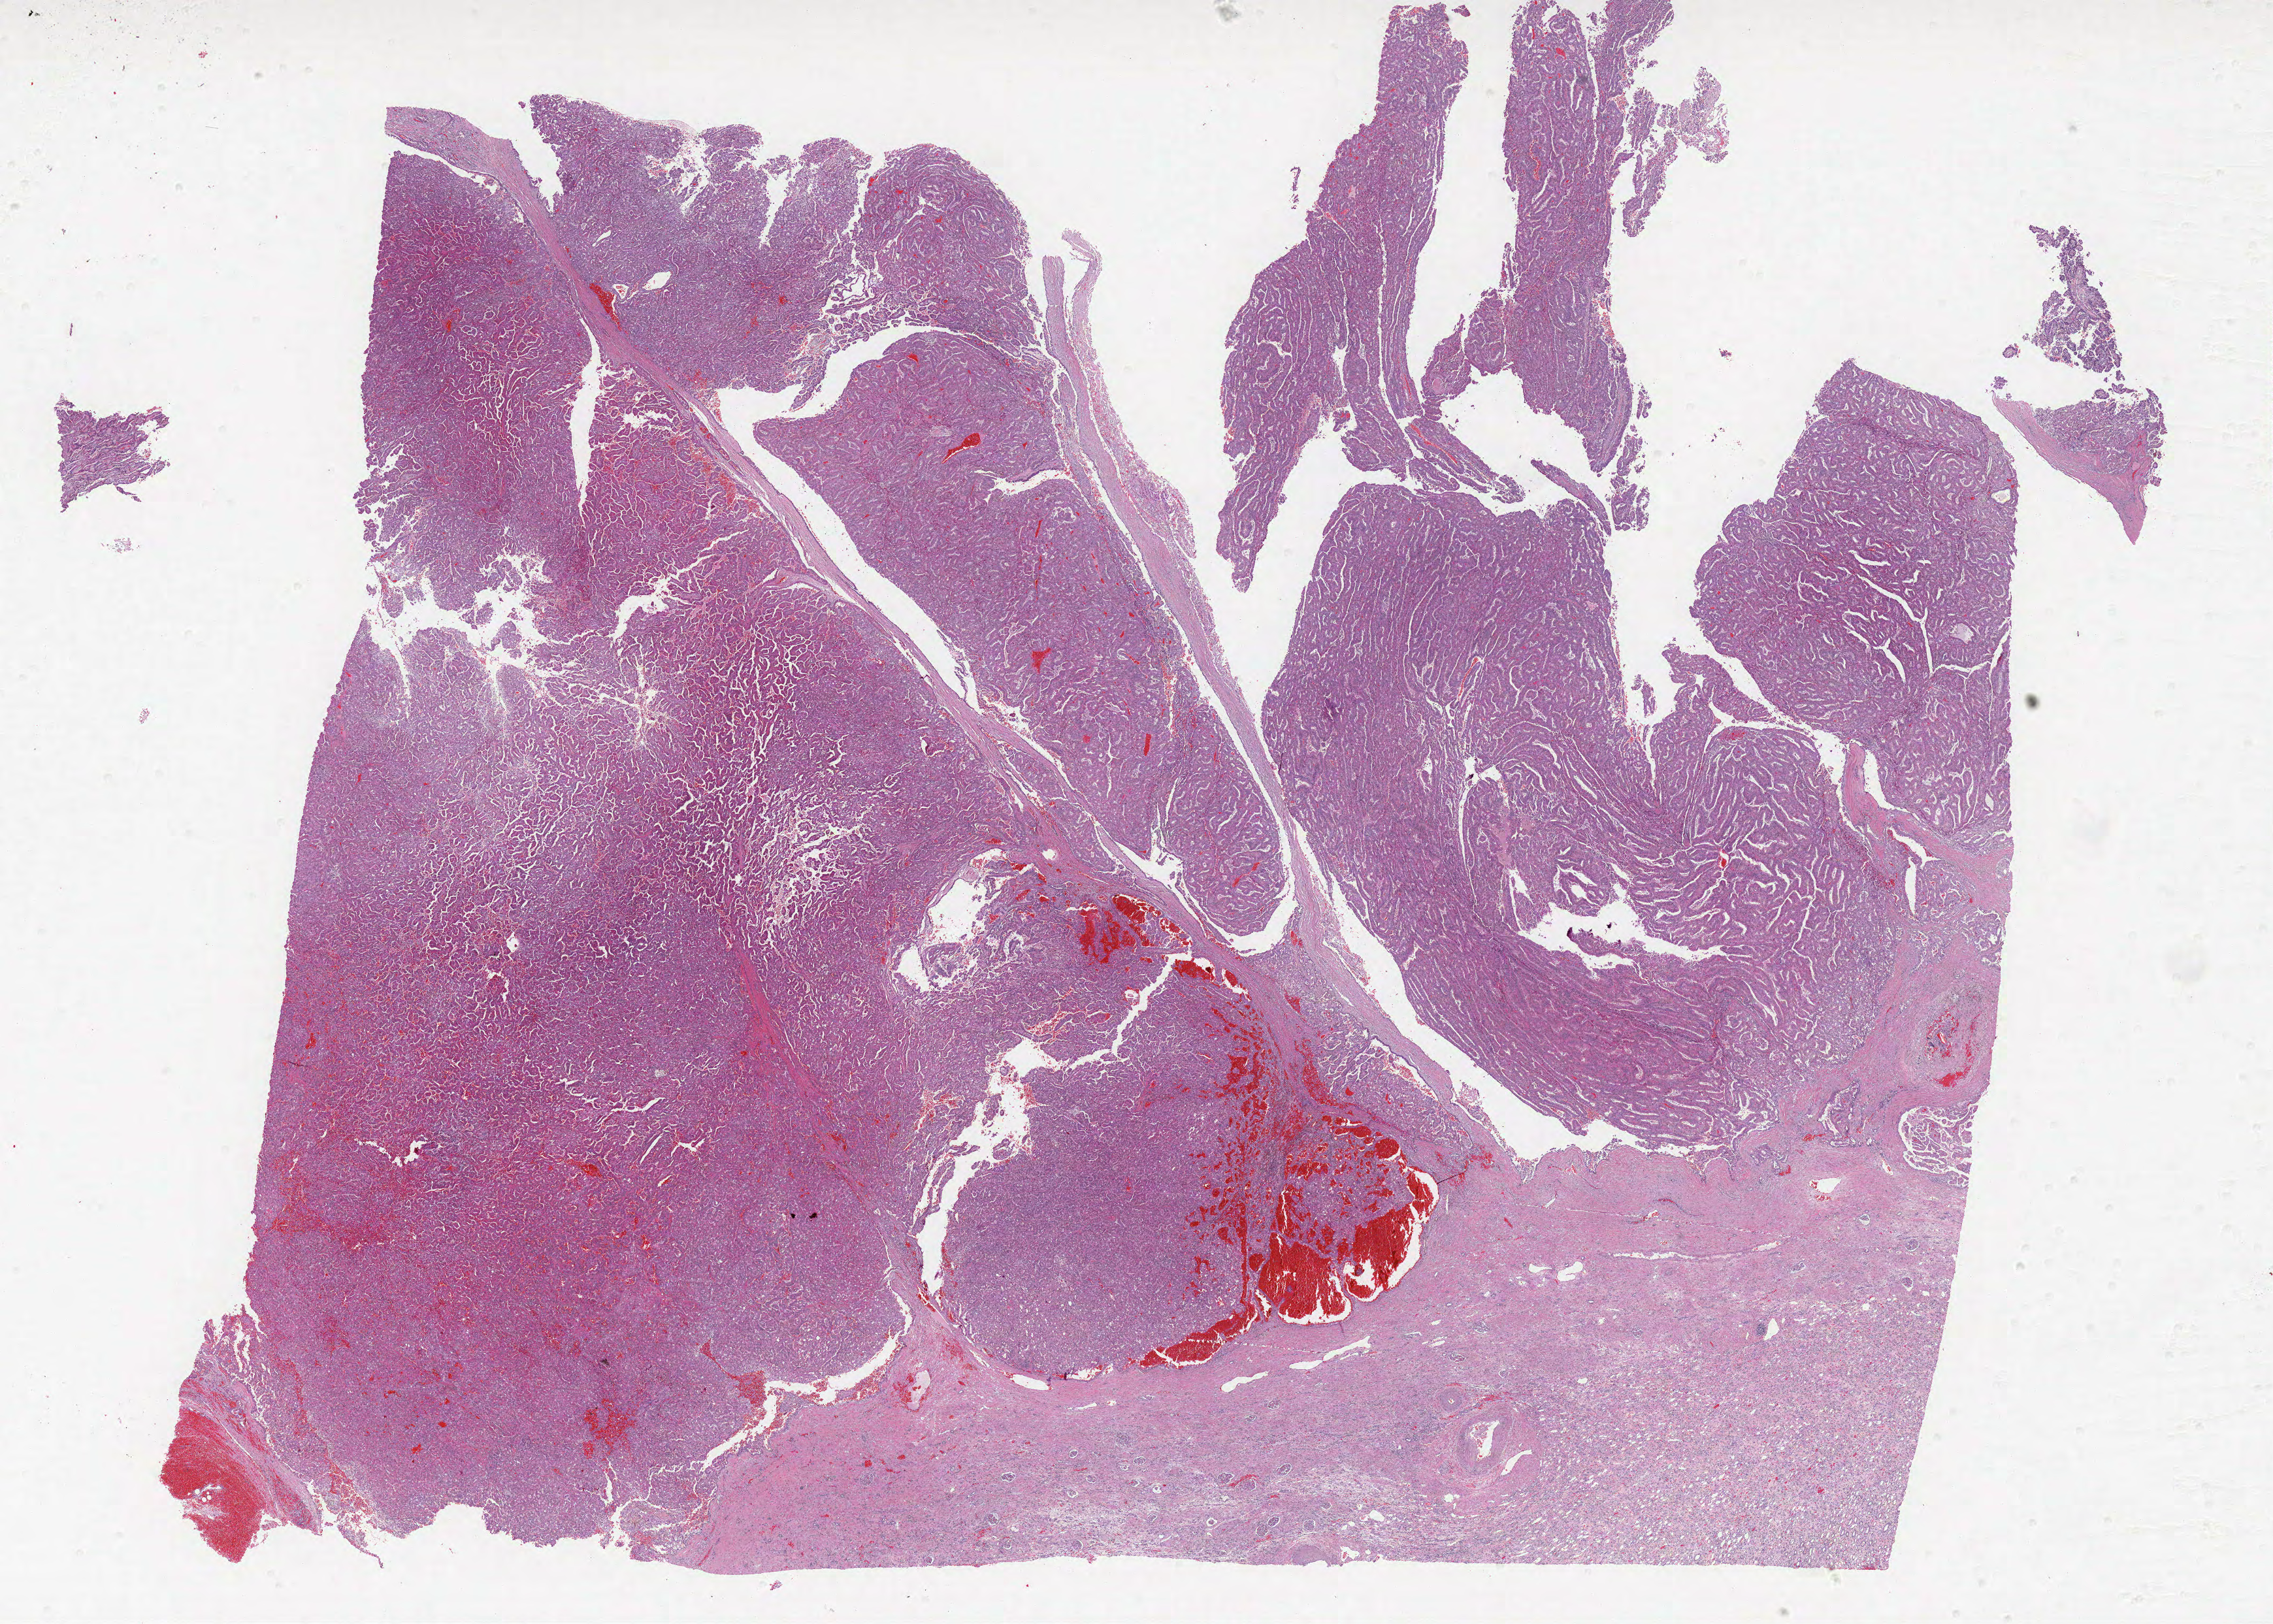
Hematoxylin and eosin (H&E) stained whole-slide image, shown as a low-resolution overview of the whole scanned area (about 27.8 x 19.9 mm, acquisition: 40x scan), formalin-fixed paraffin-embedded (FFPE) diagnostic section, sample: primary tumour, kidney. Male, age 69 years at initial diagnosis.
Laterality: right. Lymph nodes positive (case pathology): 0 of 9 examined. Pathologic diagnosis: Papillary adenocarcinoma, NOS. AJCC pathologic stage: III.